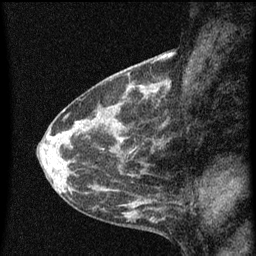
Breast MRI (dynamic contrast-enhanced), one sagittal slice; slice 23 of 60 in the series (ordered by position); dynamic contrast-enhanced series, image 2 of 3 at this slice position (ordered by acquisition); 1.5 T; TE 4.2 ms, TR 8 ms; 2 mm slice thickness; 256 × 256 image matrix, field of view 180 × 180 mm. Female patient, age 41 years.
Structures marked on this image (semi-automatically segmented with operator editing):
- analysis volume of interest (the breast-tissue region the enhancement analysis was run in; not a lesion): bounding box <130,76,157,103> (left, top, right, bottom; pixels)
- tumour enhancement mask (voxels above the 70 % enhancement threshold inside the analysis volume of interest): <140,86,149,99>